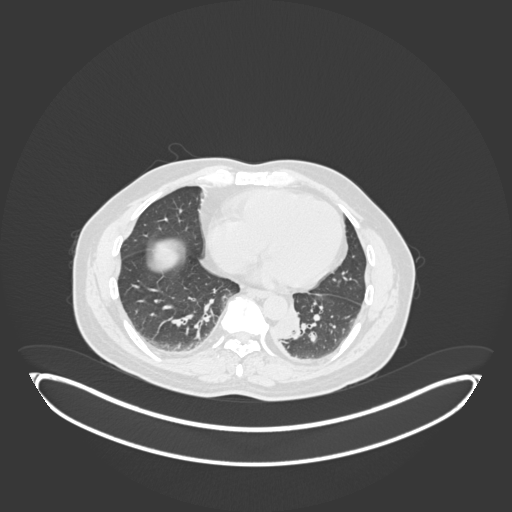
Chest CT, one axial slice. Slice 58 of 258 in the series (ordered by position). Reconstruction kernel B30f. 120 kVp. Lung window (W 1500 / L -600 HU). 512 × 512 image matrix, field of view 500 × 500 mm. Male patient, age 54 years. Case-level facts recorded for this patient, not image findings: clinical TNM (as recorded): T3 N0 M0.
Structures marked on this image (rectangle marked by the reading radiologist):
- lung tumour (recorded histology: squamous cell carcinoma): box from (x=276, y=303) to (x=305, y=346) px